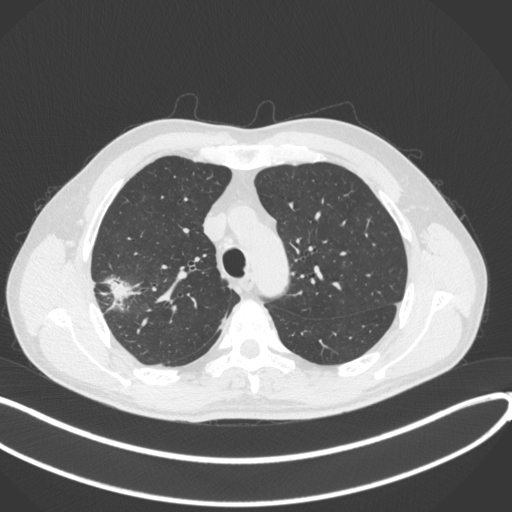
Chest CT, one axial slice. Slice 312 of 381 in the series (ordered by position). 120 kVp. Lung window (W 1500 / L -600 HU). 512 × 512 image matrix. Patient: male, 62 years. From the clinical record (not read from this slice): clinical TNM (as recorded): T1c N0 M0; histopathological grade: G2-3.
Structures marked on this image (bounding box drawn by a radiologist):
- lung tumour (recorded histology: adenocarcinoma): bounding box <100,269,147,307> (left, top, right, bottom; pixels)